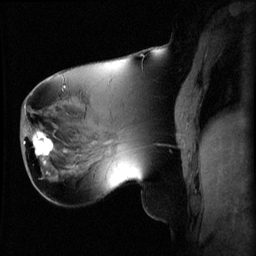
Breast MRI (dynamic contrast-enhanced), one sagittal slice; position 24 of 60 along the scan axis; 3 images stored at this slice position (order not interpretable as contrast timing); 1.5 T; TE 4.2 ms, TR 8.2 ms; 2.2 mm slice thickness; 256 × 256 image matrix, field of view 220 × 220 mm. Patient: female, 62 years.
Annotated regions visible in this slice (semi-automatically segmented with operator editing):
- analysis volume of interest (the breast-tissue region the enhancement analysis was run in; not a lesion): bounding box <26,126,59,165> (left, top, right, bottom; pixels)
- tumour enhancement mask (voxels above the 70 % enhancement threshold inside the analysis volume of interest): <32,130,53,163>